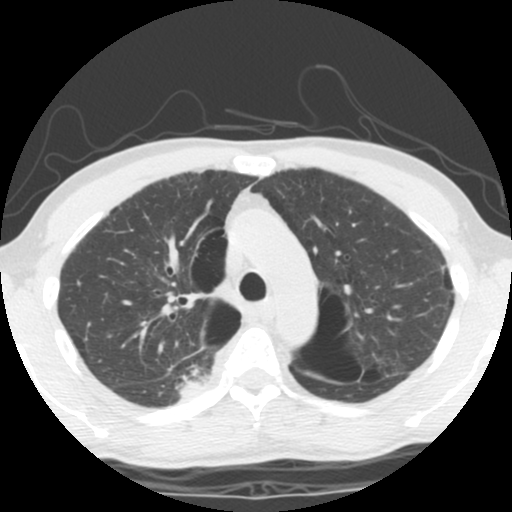
Low-dose screening chest CT, one axial slice. Slice 83 of 119 in the series (ordered by position). Lung window (W 1500 / L -600 HU). 2.5 mm slice thickness. 512 × 512 image matrix, field of view 295 × 295 mm.
Outlined on this slice (manually delineated by an expert):
- lesion 1 (tumor, upper lobe of right lung): bounding box (x1, y1, x2, y2) in pixels: (180, 367, 220, 398)